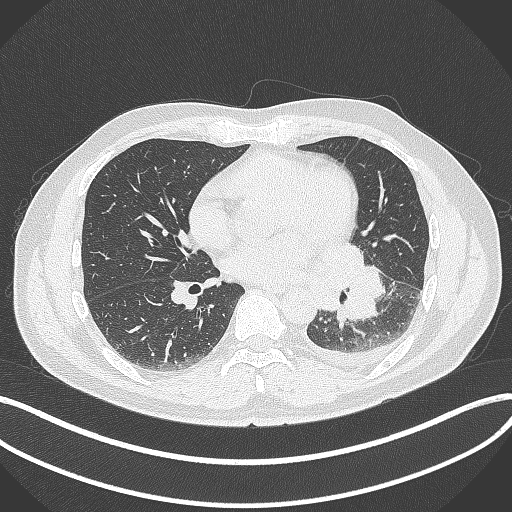
Chest CT, one axial slice; position 163 of 342 along the scan axis; reconstruction kernel B70f; lung window (W 1500 / L -600 HU); 1 mm slice thickness; 512 × 512 image matrix, field of view 400 × 400 mm. Male patient, age 58 years. Case-level facts recorded for this patient, not image findings: clinical TNM (as recorded): T3 N1 M1b; histopathological grade: G3.
Structures marked on this image (rectangle marked by the reading radiologist):
- lung tumour (recorded histology: small cell carcinoma): bounding box [x1, y1, x2, y2] px = [306, 240, 381, 327]